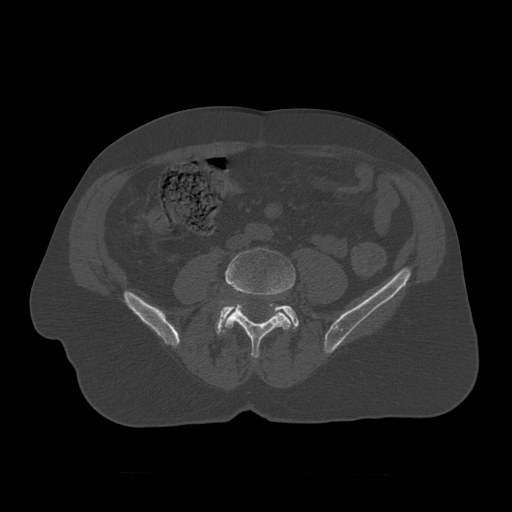
CT including the spine, one axial slice; reconstruction kernel STANDARD; bone window (W 1800 / L 400 HU); 1.25 mm slice thickness; 512 × 512 image matrix. Patient age 75 years. Case-level facts recorded for this patient, not image findings: primary cancer: prostate.
Structures marked on this image (semi-automatically segmented with operator editing):
- L4 vertebra: box from (x=221, y=248) to (x=296, y=358) px
- L5 vertebra: (x=216, y=303)–(x=300, y=336)